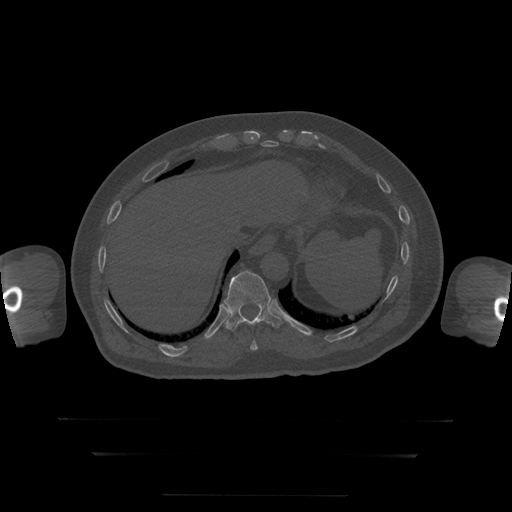
CT including the spine, one axial slice; slice 105 of 397 in the series (ordered by position); reconstruction kernel STANDARD; 120 kVp; bone window (W 1800 / L 400 HU); 1.25 mm slice thickness; 512 × 512 image matrix. Patient age 73 years. Case-level facts recorded for this patient, not image findings: primary cancer: prostate.
Outlined on this slice (semi-automatic segmentation, software-assisted and operator-edited):
- T10 vertebra: bounding box [x1, y1, x2, y2] px = [250, 341, 258, 351]
- T11 vertebra: [224, 271, 282, 331]